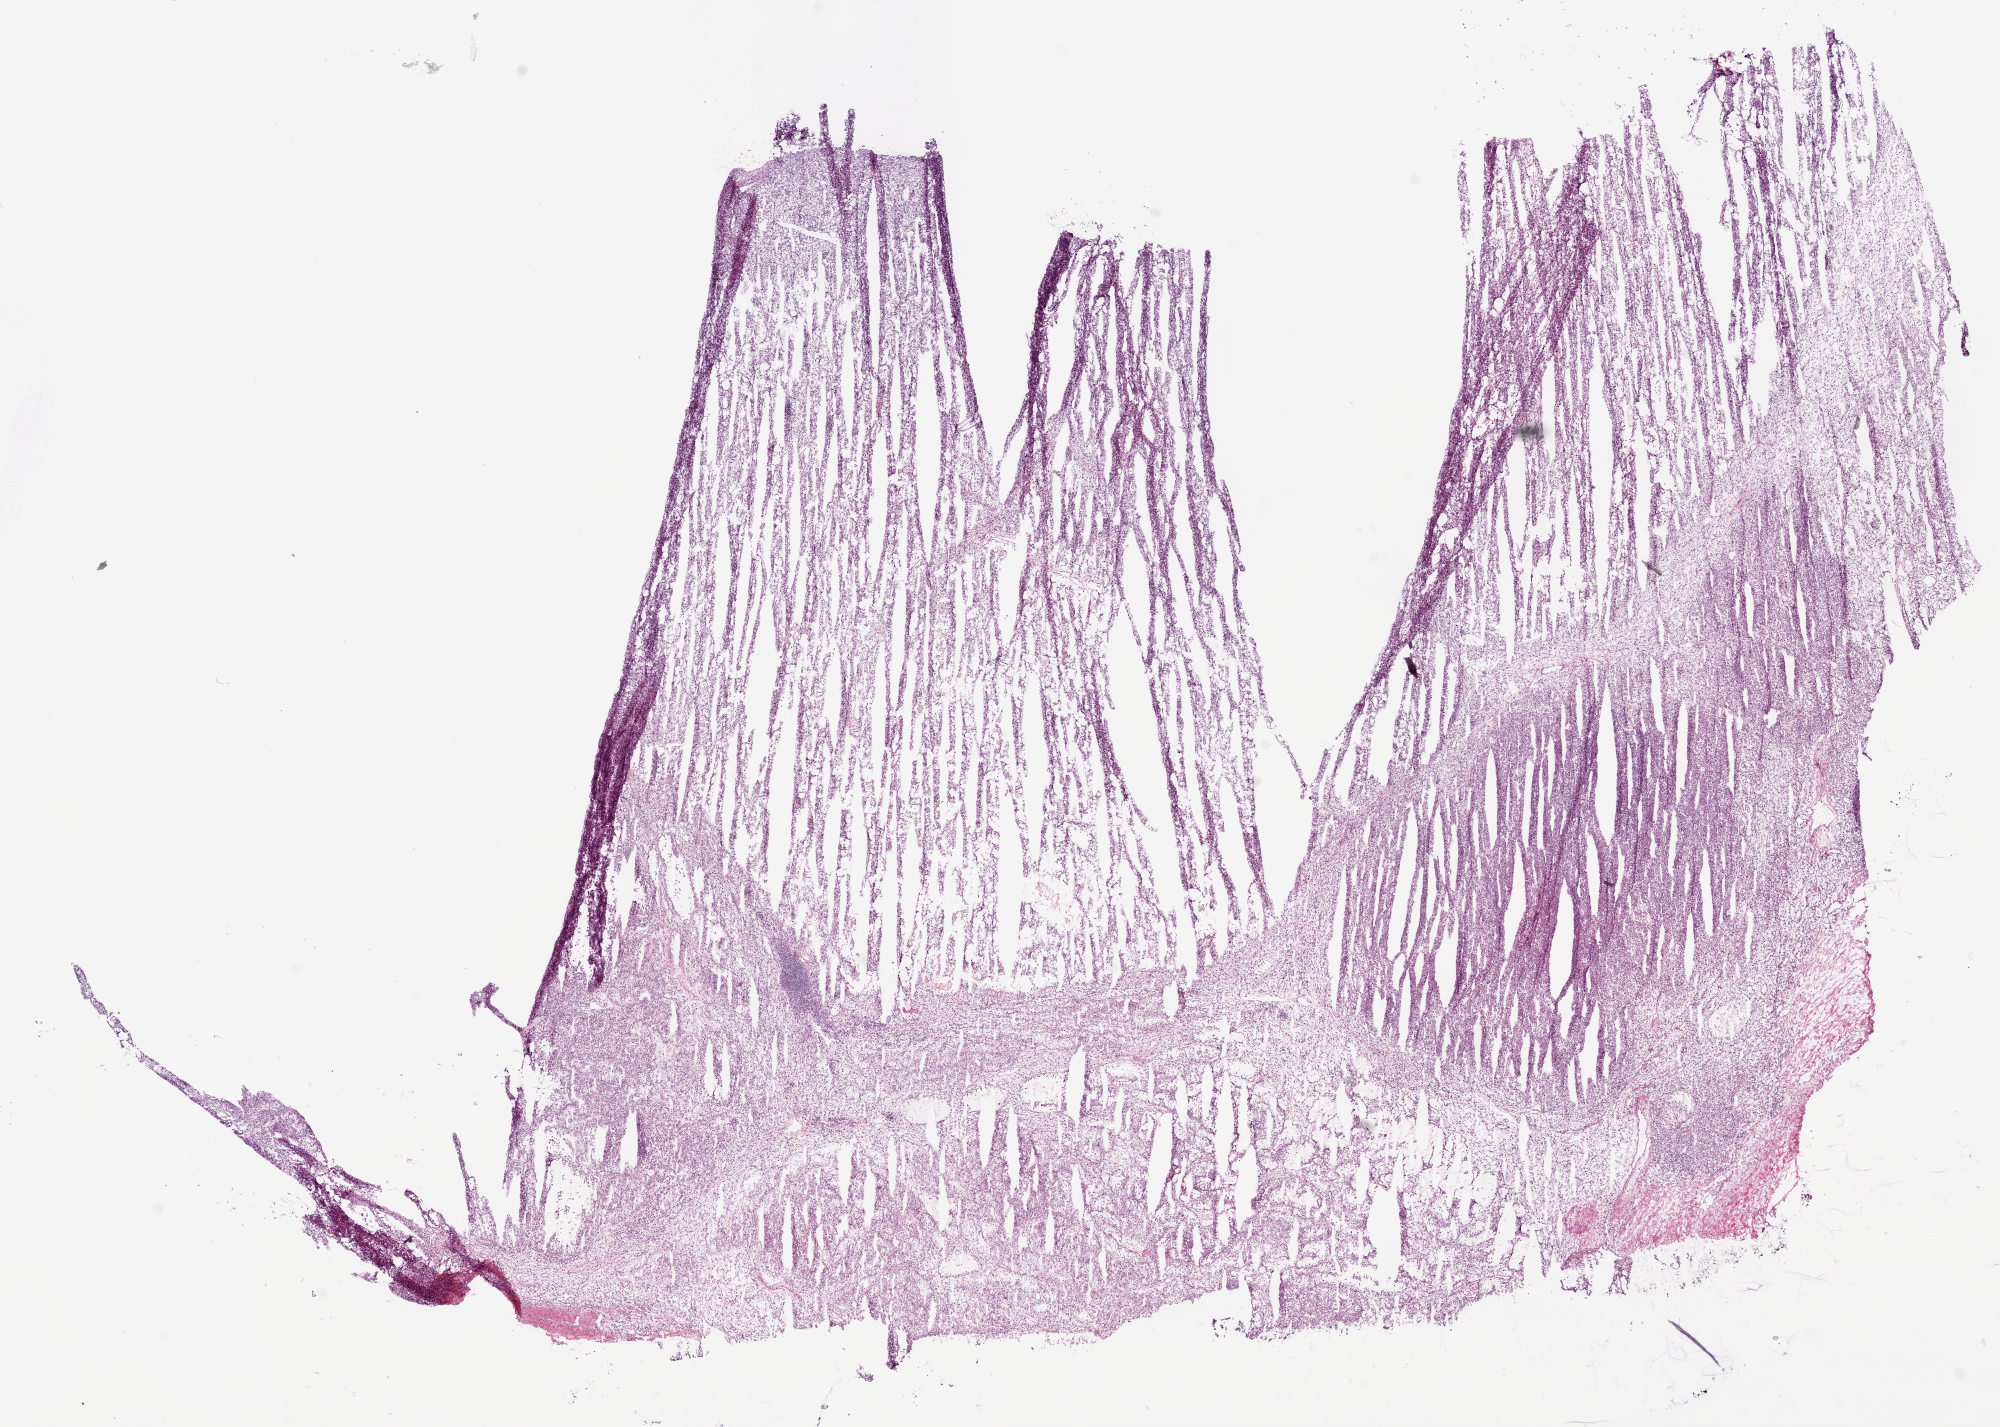
Whole-slide histology image, H&E-stained — shown as a low-resolution overview of the whole scanned area (about 16.0 x 11.5 mm, from a 20x scan); frozen section from the bottom of the tissue portion; kidney, primary tumour sample. Male patient; age at initial diagnosis 57 years. Histologic grade: G2 (moderately differentiated). Slide review estimates, as recorded: tumour cells 90%, tumour nuclei 80%, normal cells 0%, stromal cells 10%, necrosis 0%.
- histologic diagnosis: Clear cell adenocarcinoma, NOS
- laterality: right
- AJCC pathologic stage: I